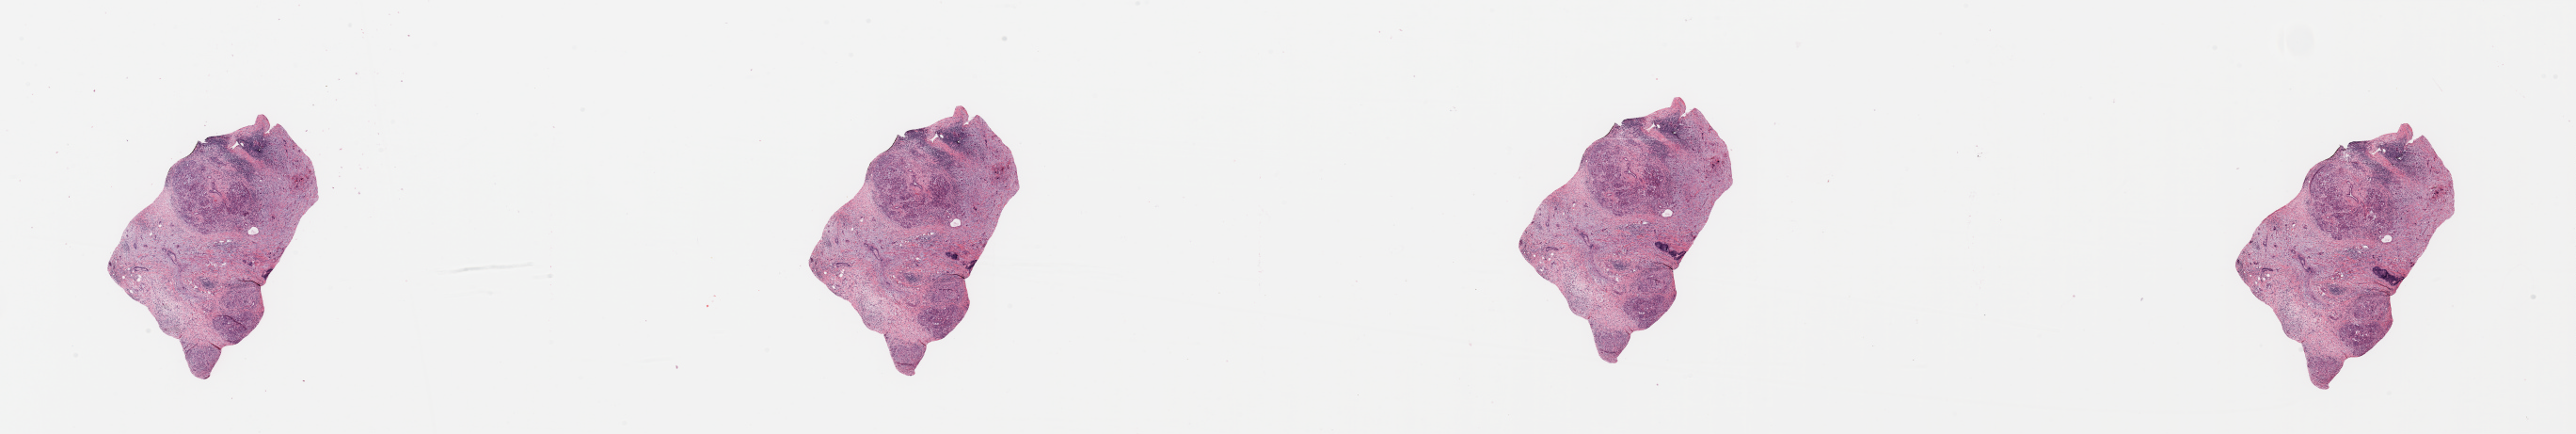
H&E whole-slide image, low-resolution overview of the scanned area, about 43.3 x 7.3 mm (from a 20x scan), tumour tissue sample, sampled site: pancreas. Patient: male, age 65 years.
Histologic diagnosis: Infiltrating duct carcinoma, NOS.